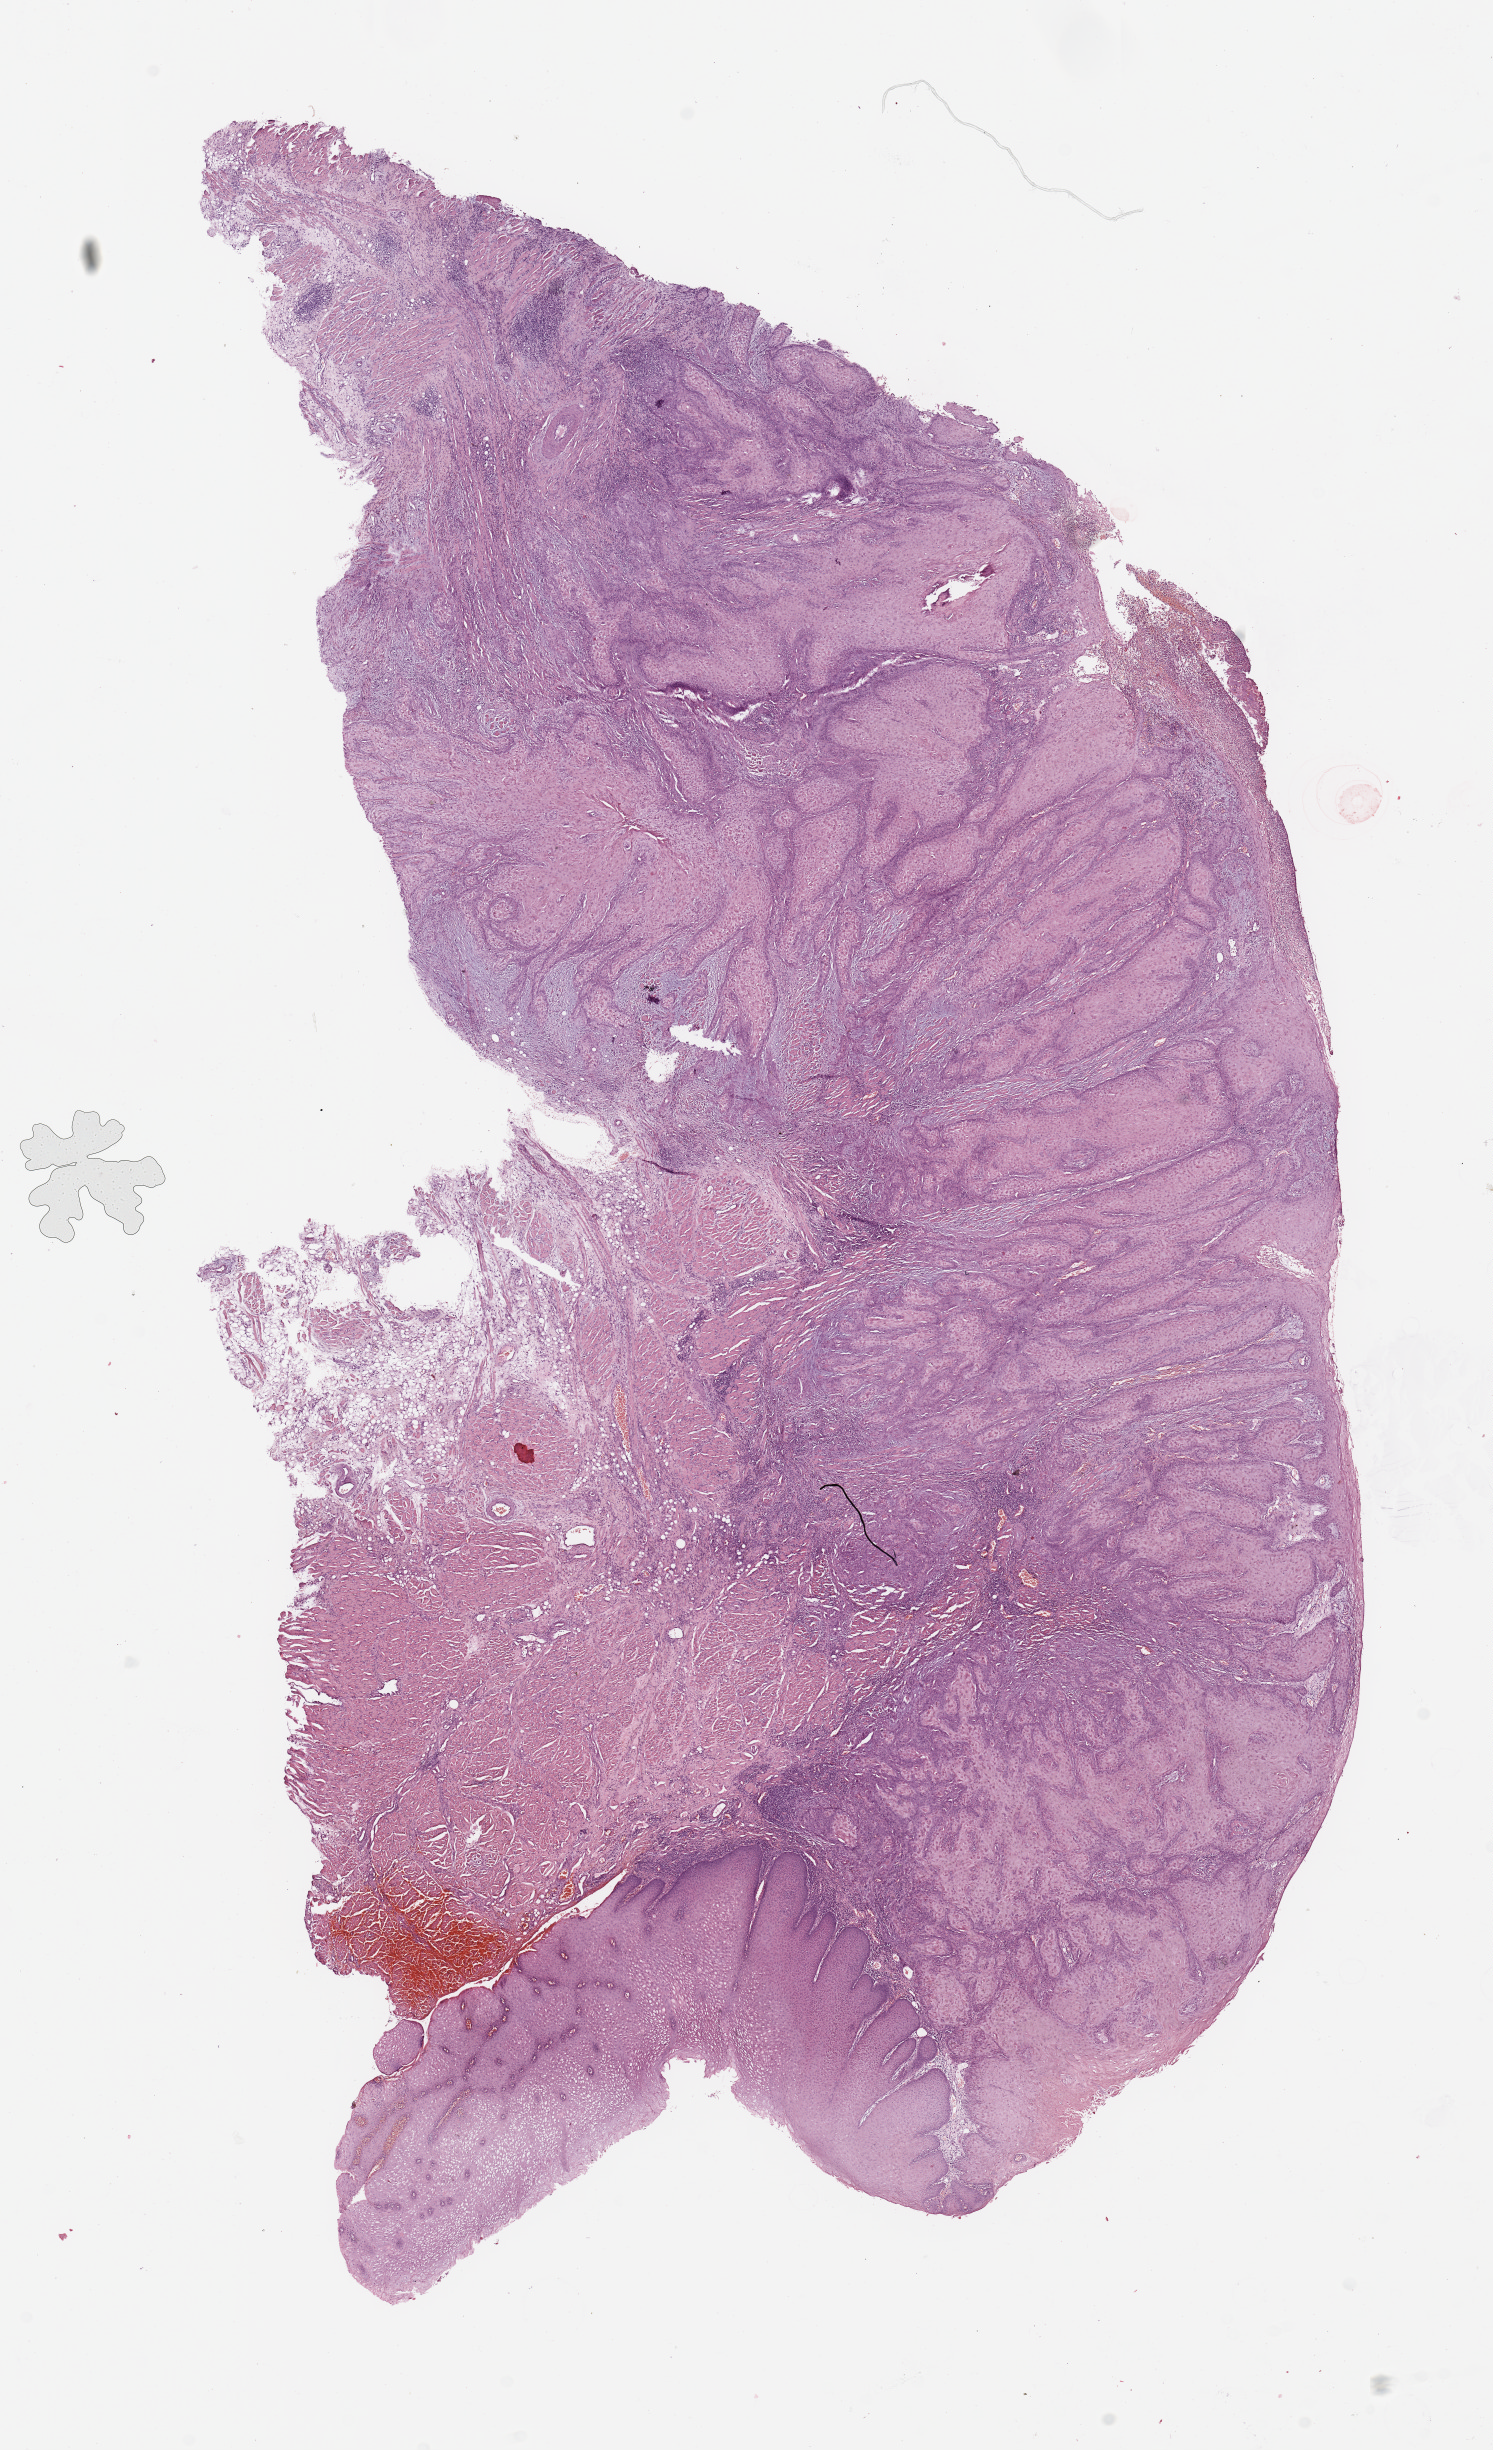
Whole-slide histology image, H&E — shown as a low-resolution overview of the whole scanned area (about 11.8 x 19.4 mm, slide scanned at 20x). Head and neck, tissue type not recorded. Patient: male, age 54 years.
Patient diagnosis: Squamous cell carcinoma, NOS (tongue, NOS).